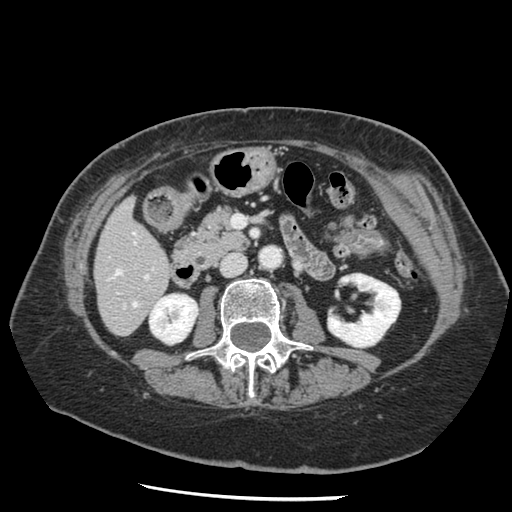
Contrast-enhanced abdominal CT, one axial slice; 120 kVp; intravenous contrast given; soft-tissue window (W 400 / L 40 HU); 512 × 512 image matrix. Female patient, age 85 years. Case-level facts recorded for this patient, not image findings: diagnosis: colorectal cancer liver metastases, imaged before liver resection; multiple liver metastases: no; largest metastasis: 0.9 cm; disease in both lobes: no.
Outlined on this slice (manually delineated by an expert):
- hepatic veins: bounding box [x1, y1, x2, y2] px = [115, 270, 137, 307]
- liver: [95, 201, 171, 335]
- planned liver remnant (the part of the liver to remain after resection): [96, 201, 171, 329]